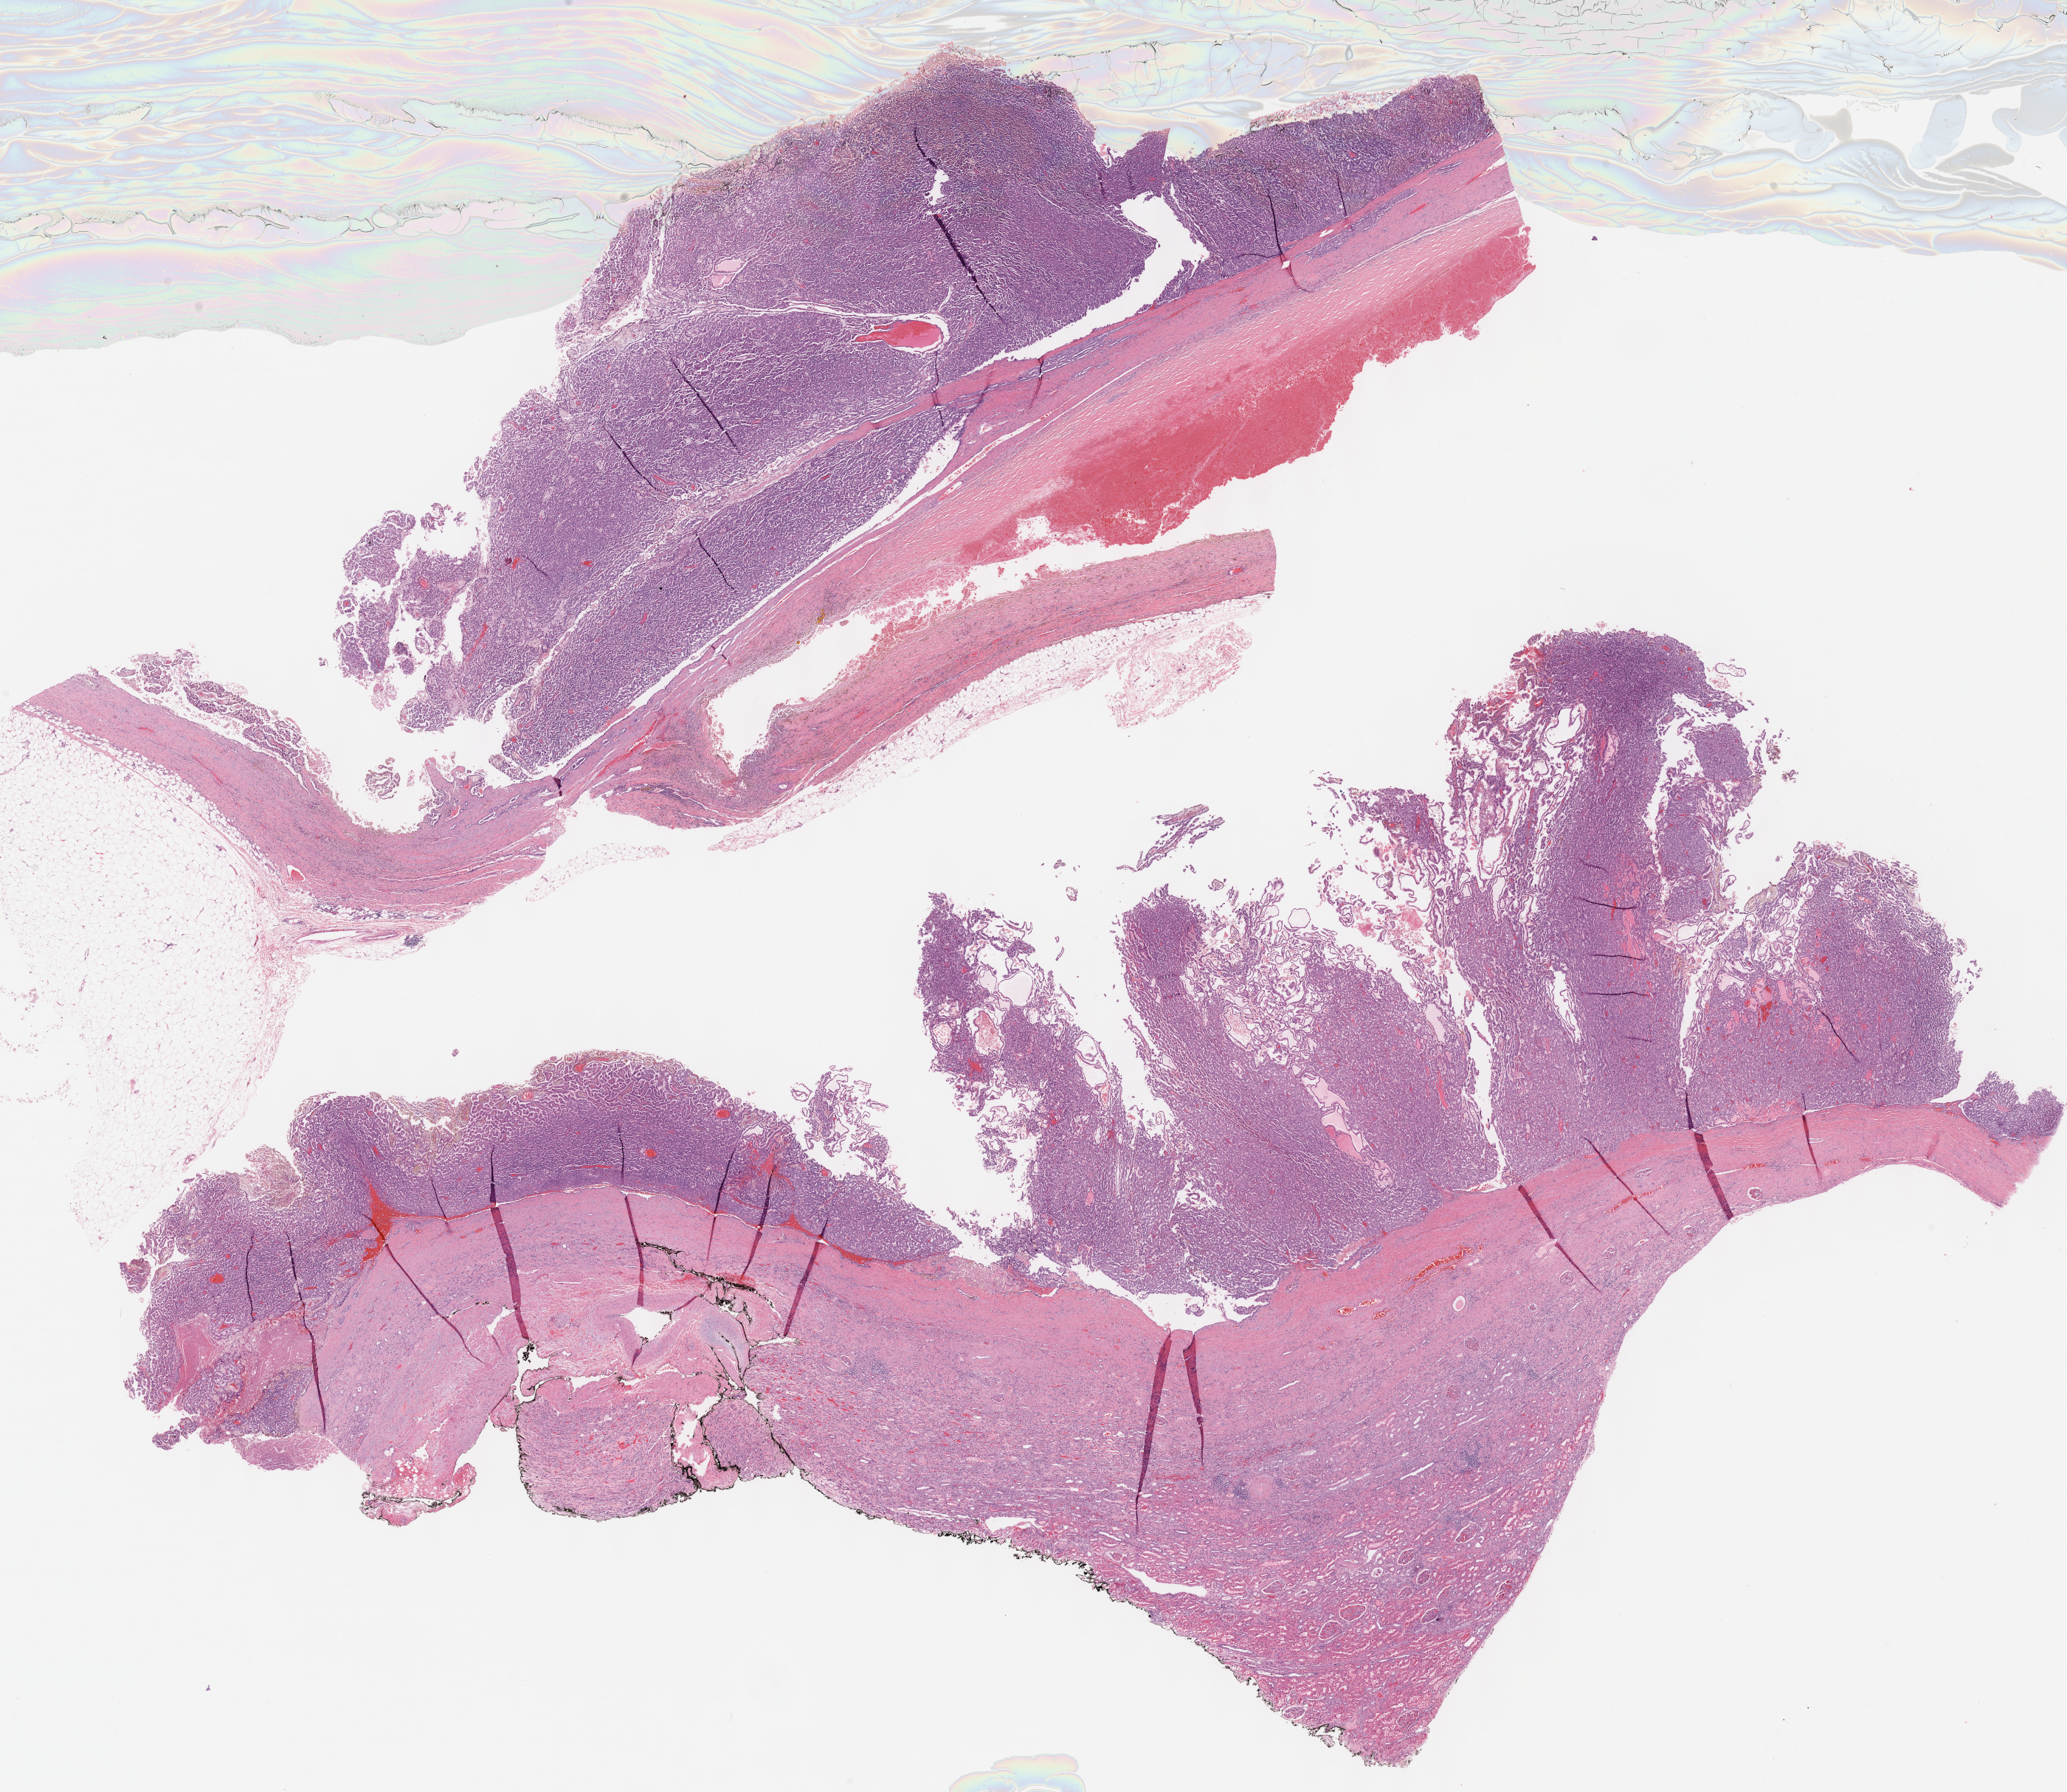
H&E-stained whole-slide image — shown as a low-resolution overview of the whole scanned area (about 22.6 x 19.6 mm, slide scanned at 40x). Formalin-fixed paraffin-embedded (FFPE) diagnostic section. Primary tumour sample from the kidney. Patient: male, age at initial diagnosis 60 years.
Pathologic diagnosis: Papillary adenocarcinoma, NOS. AJCC pathologic stage: I (6th edition). Laterality: left.